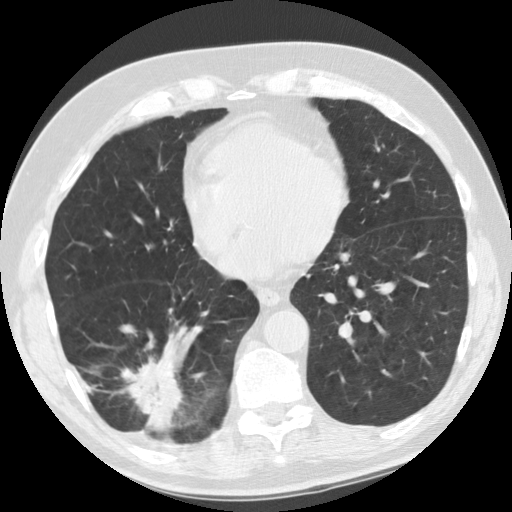
Low-dose screening chest CT, one axial slice; position 45 of 135 along the scan axis; reconstruction kernel STANDARD; lung window (W 1500 / L -600 HU); 2.5 mm slice thickness; 512 × 512 image matrix, field of view 340 × 340 mm.
Annotated regions visible in this slice (manually delineated by an expert):
- lesion 1 (tumor, lower lobe of right lung): box from (x=121, y=349) to (x=184, y=434) px